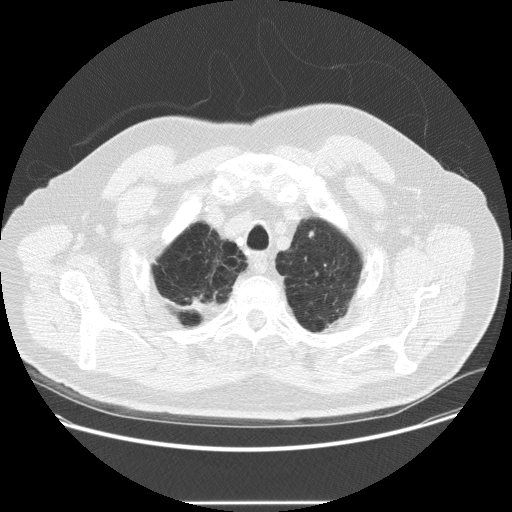
Chest CT (low-dose screening protocol), one axial image. Second screening round (one year after baseline). Lung window (W 1500 / L -600 HU). 2.5 mm slice thickness. Standard (soft-tissue) reconstruction kernel (STANDARD). 120 kVp. Slice 45 of 265 in the series. Male participant, aged 64 years at enrolment. Current smoker at enrolment.
Expert-annotated lung lesion, bounding box (x1, y1, x2, y2) in pixels: (298, 223, 326, 250). Reader record for this screening exam (exam-level; its link to the box is not recorded): non-calcified nodule or mass ≥4 mm, left upper lobe, 5 × 3 mm, smooth margins, soft tissue attenuation, pre-existing on the prior screen: no. Official screen result: positive, other. Later outcome: lung cancer diagnosed 300 days after this screen — adenocarcinoma, NOS, left upper lobe, poorly differentiated (G3), stage IA (AJCC 6th edition), 8 mm at pathology.